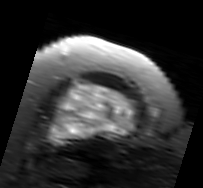
MRI of an extremity soft-tissue mass, one axial slice; slice 59 of 91 in the series (ordered by position); T2-weighted fat-saturated; MR volume resampled by the dataset authors to the PET/CT grid (not the native acquisition matrix); 3.27 mm slice thickness; 203 × 188 image matrix, field of view 198 × 184 mm. Female patient. From the clinical record (not read from this slice): histological type: malignant solitary fibrous tumor; grade: intermediate; site of the primary tumour: right thigh.
Outlined on this slice (expert contour drawn on MRI and transferred to this co-registered scan by the dataset authors):
- gross tumour volume including surrounding oedema: bounding box [x1, y1, x2, y2] px = [47, 79, 141, 148]
- gross tumour volume (mass): [49, 83, 137, 146]